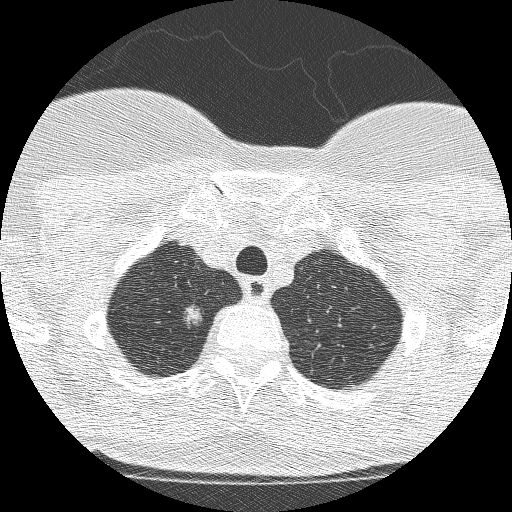
Low-dose screening chest CT, axial slice, second screening round (one year after baseline), lung window (W 1500 / L -600 HU). Female, age 61 years at enrolment. Current smoker at enrolment.
Lesion marked by an expert reader, bounding box <167,297,215,335> (left, top, right, bottom; pixels). Screening reader's record for this exam (one nodule recorded; not confirmed to be the boxed lesion): non-calcified nodule or mass ≥4 mm, right upper lobe, 11 × 8 mm, poorly defined margins, mixed attenuation, pre-existing on the prior screen: yes; interval growth: yes. Participant outcome: lung cancer diagnosed 28 days after this screen — adenocarcinoma, NOS, right upper lobe, poorly differentiated (G3), 12 mm at pathology.